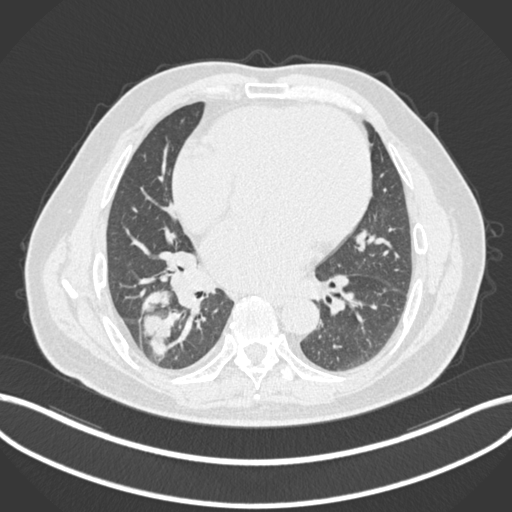
Chest CT, one axial slice. Slice 79 of 200 in the series (ordered by position). 120 kVp. Lung window (W 1500 / L -600 HU). 1 mm slice thickness. 512 × 512 image matrix, field of view 400 × 400 mm. Male patient, age 59 years.
Annotated regions visible in this slice (rectangle marked by the reading radiologist):
- lung tumour (recorded histology: adenocarcinoma): bounding box (x1, y1, x2, y2) in pixels: (137, 289, 179, 361)